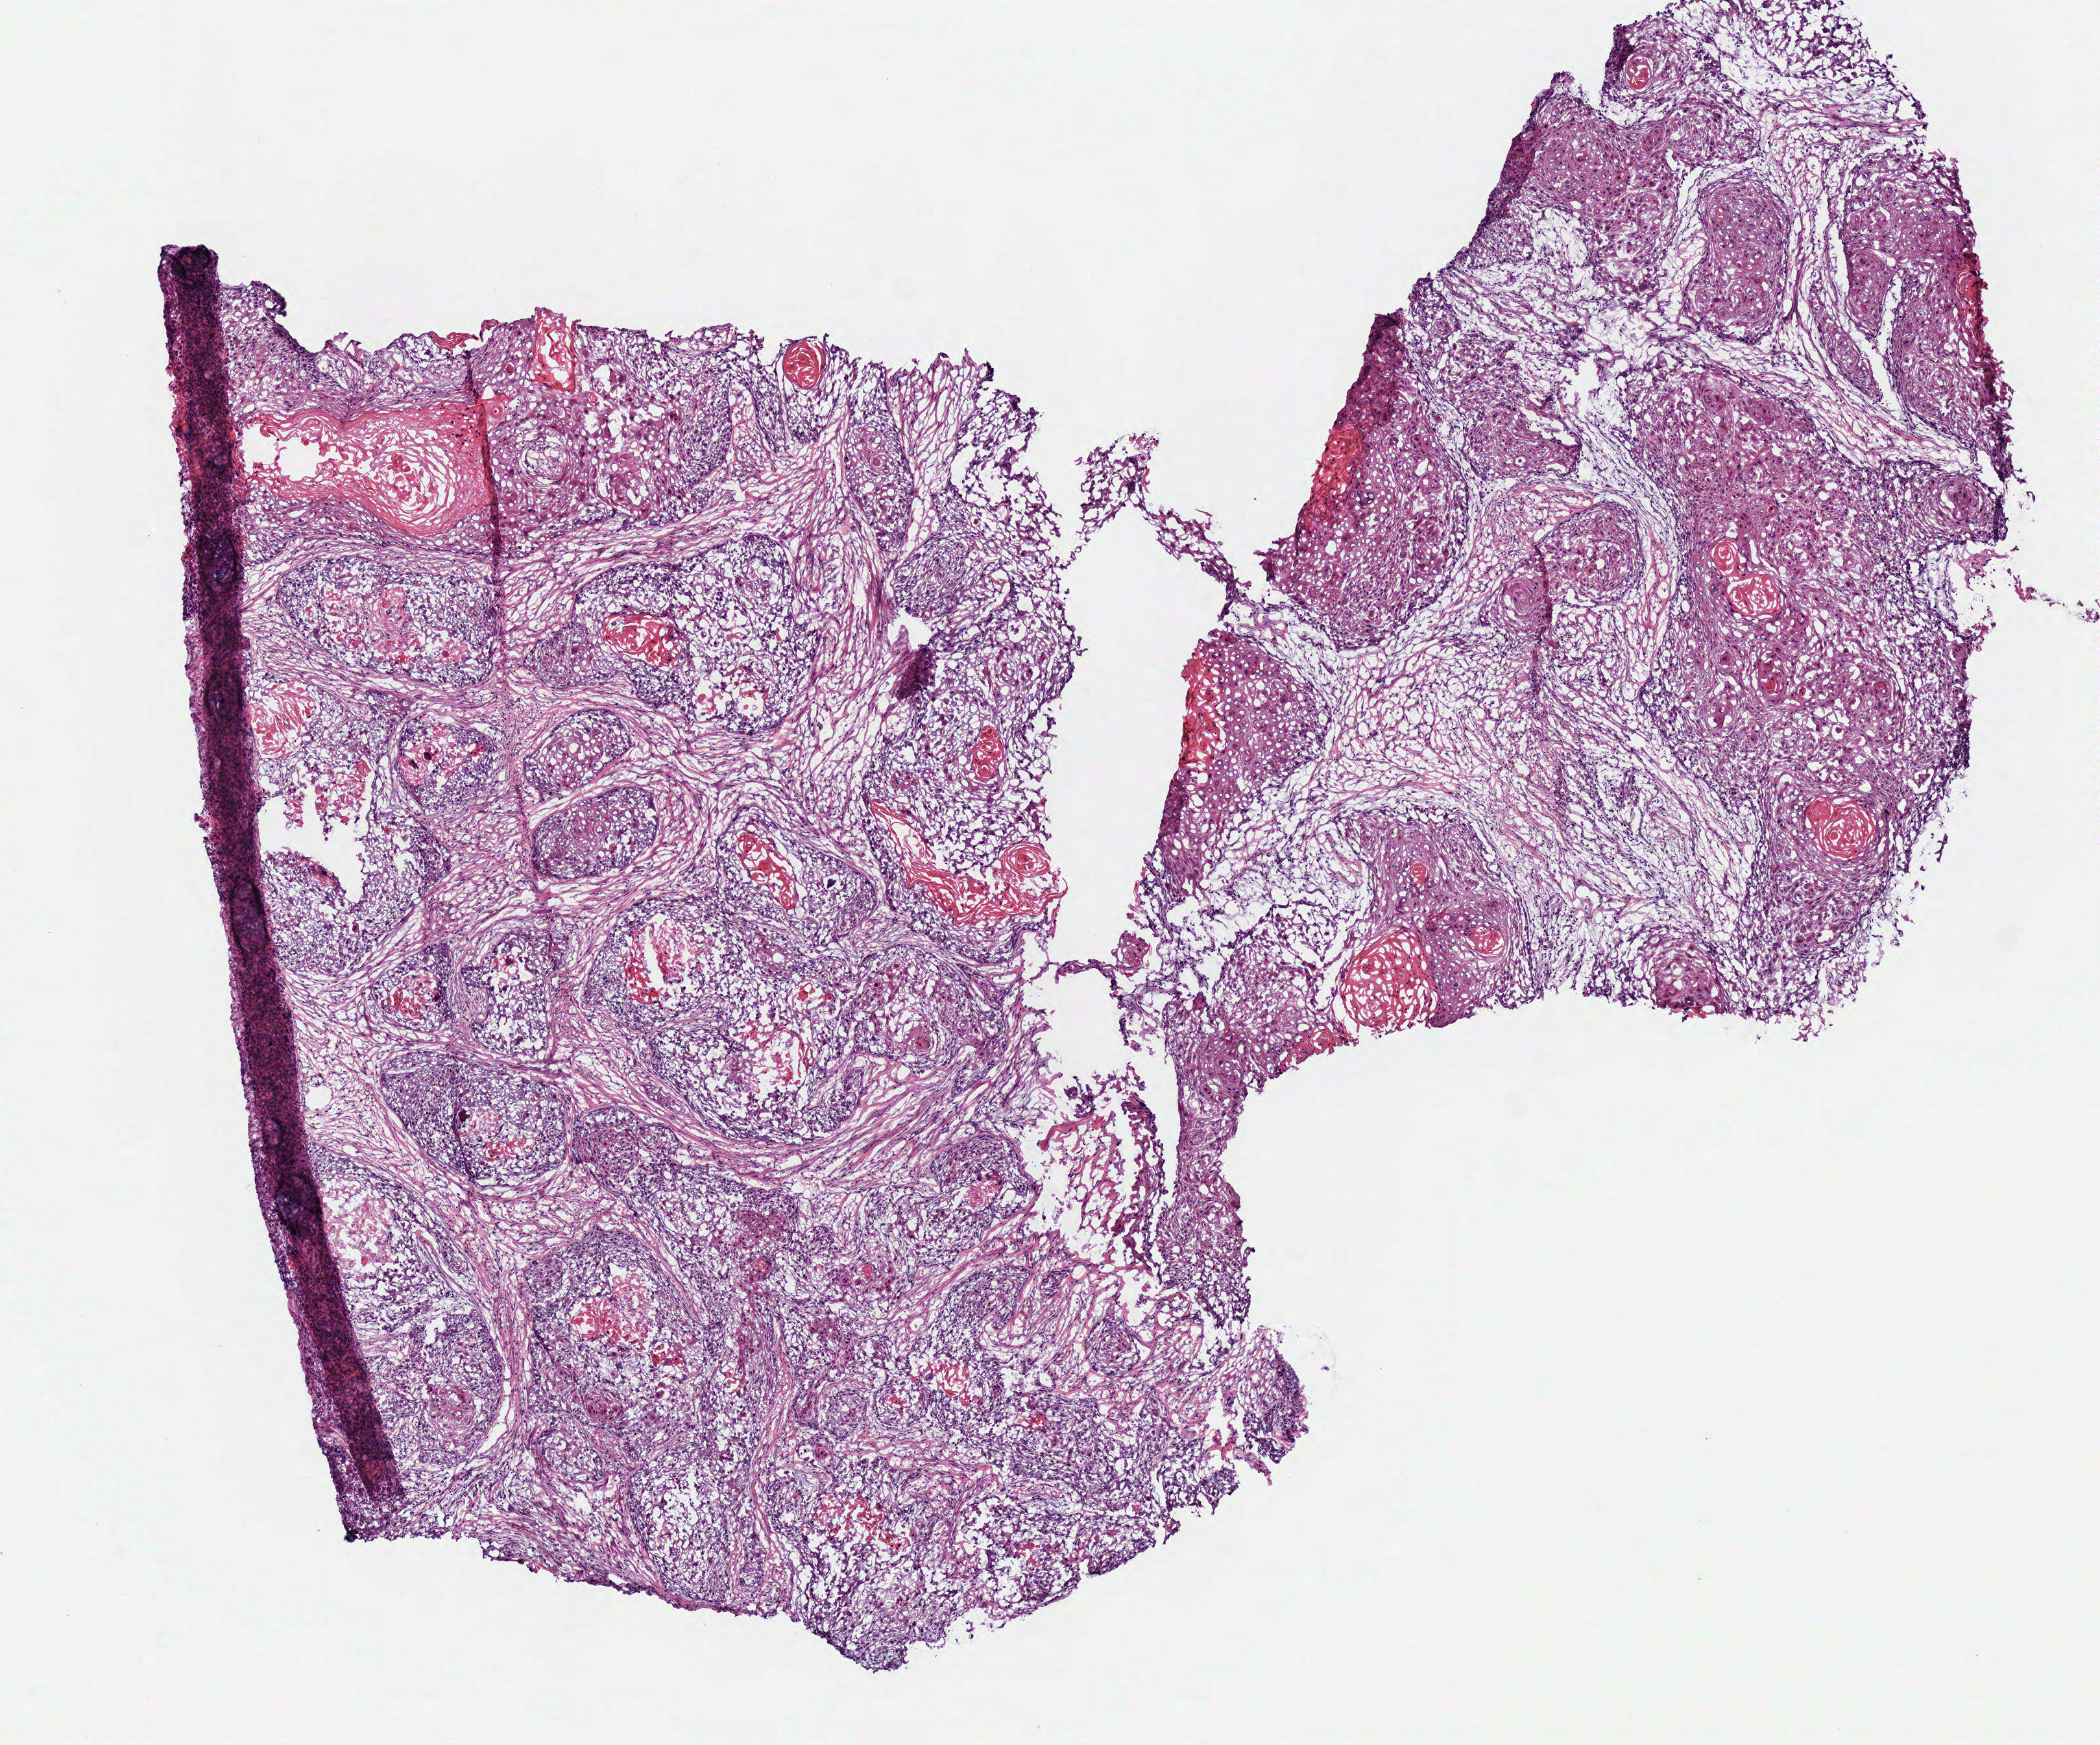
H&E-stained whole-slide image — shown as a low-resolution overview of the whole scanned area (about 6.4 x 5.3 mm, slide scanned at 40x); frozen section from the top of the tissue portion; sample: primary tumour, head and neck. Patient: male, age at initial diagnosis 67 years. Histologic grade: G2 (moderately differentiated). Slide review estimates, as recorded: tumour cells 90%, tumour nuclei 75%, normal cells 0%, stromal cells 10%, necrosis 0%.
TNM: T4a N0. Lymph nodes positive (case pathology): 0 of 37 examined. Diagnosis: Squamous cell carcinoma, NOS (overlapping lesion of lip, oral cavity and pharynx). AJCC pathologic stage: IVA.